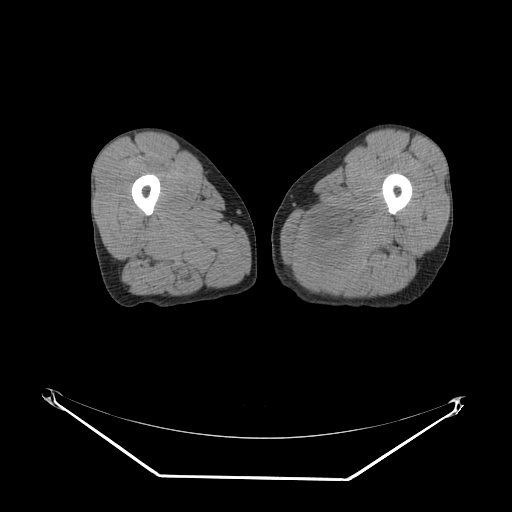
CT of an extremity soft-tissue mass (from a PET/CT study), one axial slice. Position 14 of 267 along the scan axis. Reconstruction kernel SOFT. 140 kVp. Soft-tissue window (W 400 / L 40 HU). 512 × 512 image matrix, field of view 500 × 500 mm. Male patient. Case-level facts recorded for this patient, not image findings: histological type: pleiomorphic liposarcoma; grade: high; site of the primary tumour: left thigh.
Outlined on this slice (expert contour drawn on MRI and transferred to this co-registered scan by the dataset authors):
- gross tumour volume including surrounding oedema: box from (x=308, y=203) to (x=375, y=277) px
- gross tumour volume (mass): (x=320, y=247)–(x=355, y=271)